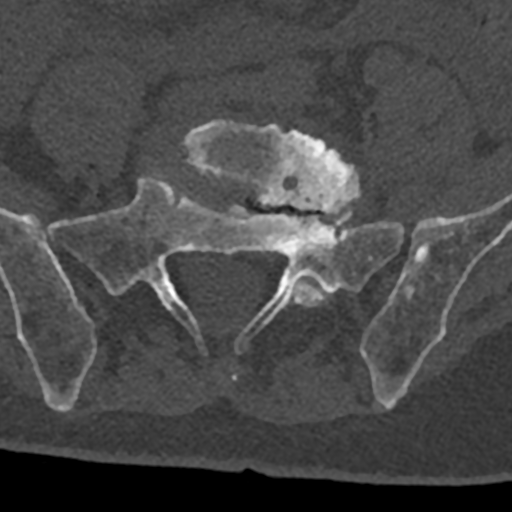
CT including the spine, one axial slice. Position 165 of 797 along the scan axis. Reconstruction kernel Br40s/3. Bone window (W 1800 / L 400 HU). 0.5 mm slice thickness. 512 × 512 image matrix. Male patient, age 74 years. Case-level facts recorded for this patient, not image findings: primary cancer: renal; vertebrae with lytic lesions (as recorded): T10, L1, L2, L3, L4, L5.
Annotated regions visible in this slice (semi-automatic segmentation, software-assisted and operator-edited):
- L5 vertebra: bounding box <176,121,360,307> (left, top, right, bottom; pixels)